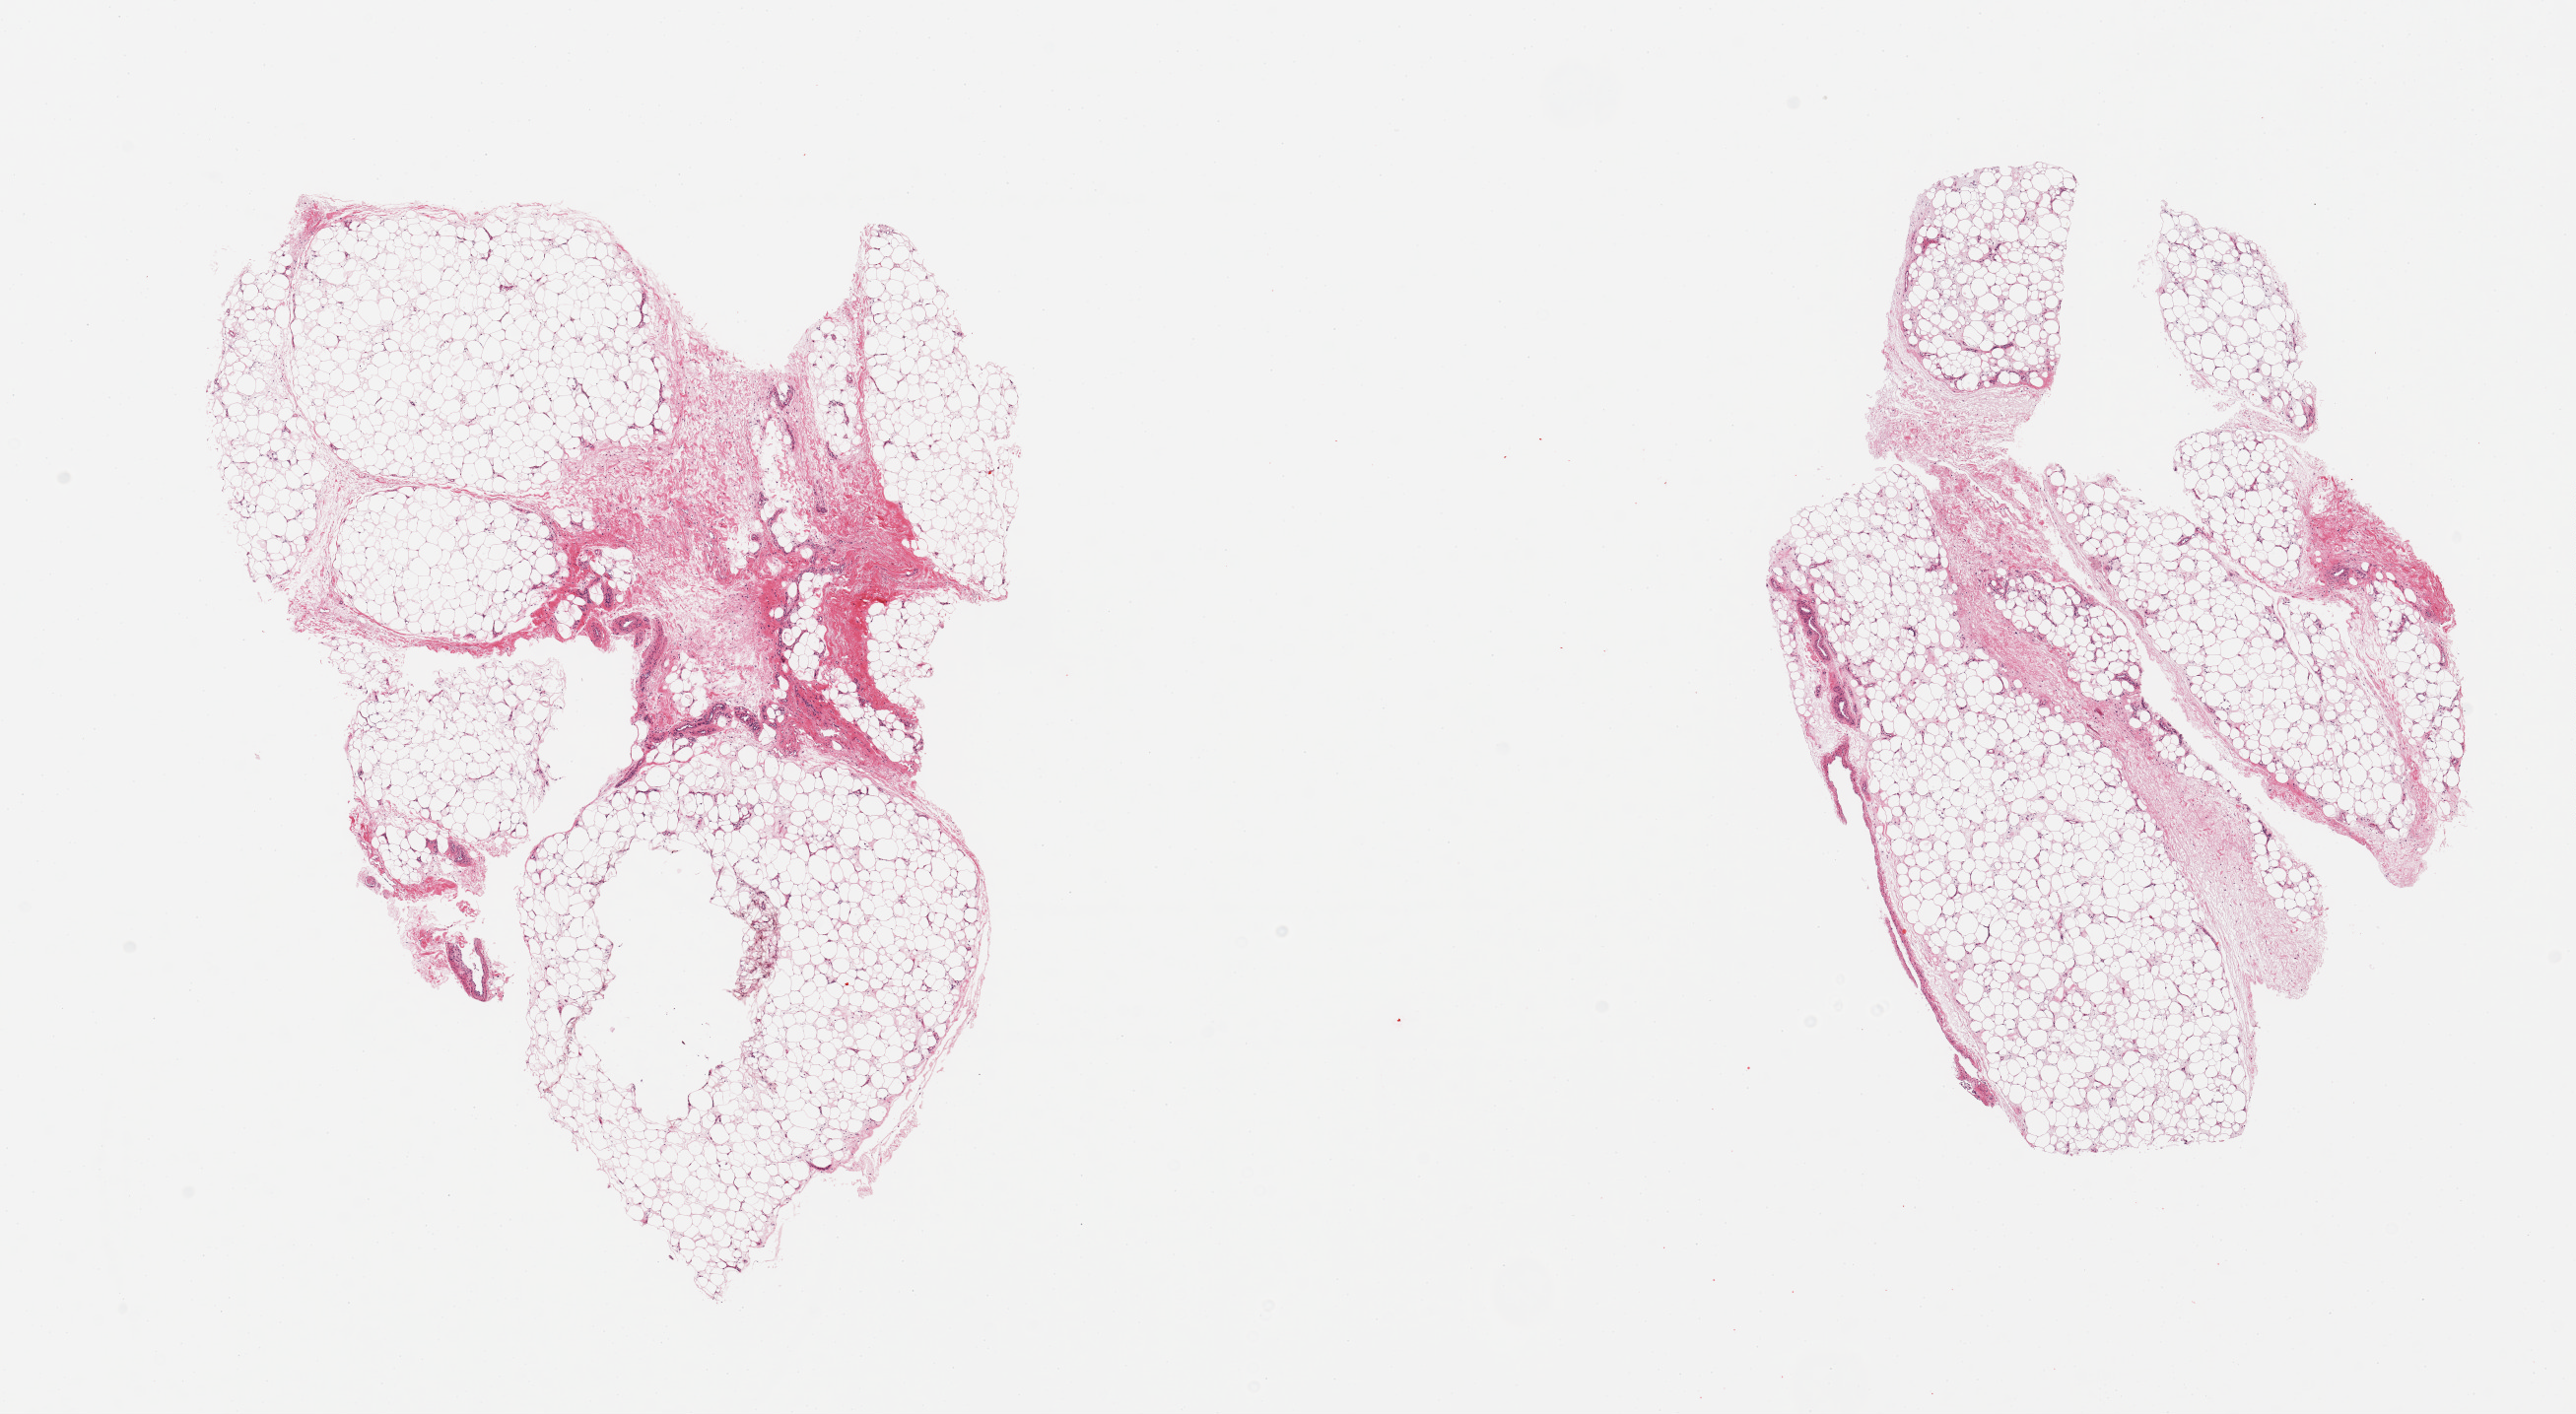
Digitized haematoxylin and eosin-stained section — whole scanned area (about 20.7 x 11.3 mm, acquisition: 20x scan) shown as a low-resolution overview. PAXgene-fixed, paraffin-embedded tissue. Sampled site (target tissue): adipose tissue. Tissue donor sample.
• pathologist's review note for this sample: 2 pieces, ~20 % fascia/vascular elements